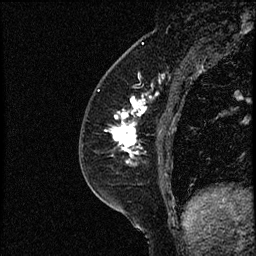
Breast MRI (dynamic contrast-enhanced), one sagittal slice; position 25 of 52 along the scan axis; dynamic contrast-enhanced study with each time point stored as its own series, time point 2 of 3 at this slice position (early post-contrast, ordered by acquisition time); 1.5 T; TE 4.2 ms, TR 17.6 ms; 2 mm slice thickness; 256 × 256 image matrix, field of view 200 × 200 mm. Patient: female, 49 years. From the clinical record (not read from this slice): setting: breast cancer imaged before/during neoadjuvant chemotherapy; receptor status: HER2-positive.
Structures marked on this image (semi-automatically segmented with operator editing):
- analysis volume of interest (the breast-tissue region the enhancement analysis was run in; not a lesion): bounding box (x1, y1, x2, y2) in pixels: (85, 65, 182, 175)
- tumour enhancement mask (voxels above the 100 % enhancement threshold inside the analysis volume of interest): (107, 97, 154, 159)